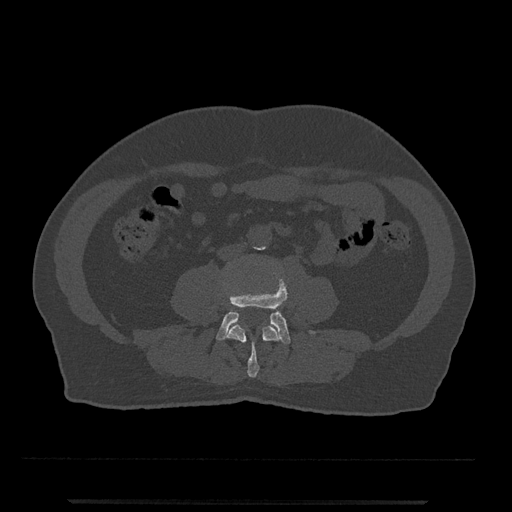
CT including the spine, one axial slice. Slice 166 of 797 in the series (ordered by position). Reconstruction kernel Br40s/3. 120 kVp. Bone window (W 1800 / L 400 HU). 0.5 mm slice thickness. 512 × 512 image matrix, field of view 419 × 419 mm. Patient: male, 63 years. Case-level facts recorded for this patient, not image findings: primary cancer: prostate.
Outlined on this slice (semi-automatic segmentation, software-assisted and operator-edited):
- L3 vertebra: bounding box (x1, y1, x2, y2) in pixels: (226, 324, 280, 378)
- L4 vertebra: (216, 276, 315, 345)